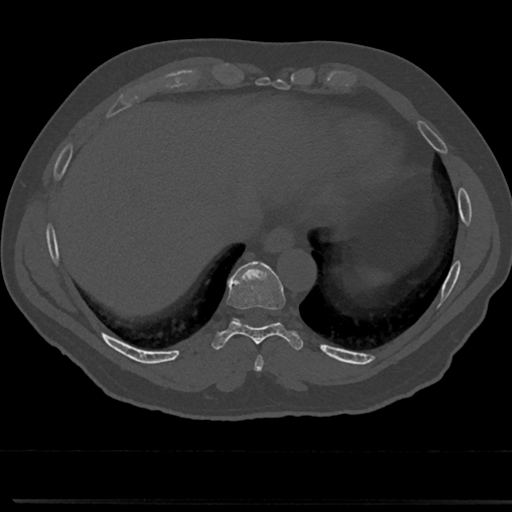
CT including the spine, one axial slice. 120 kVp. Bone window (W 1800 / L 400 HU). 0.5 mm slice thickness. 512 × 512 image matrix, field of view 355 × 355 mm. Patient: male, 61 years. Case-level facts recorded for this patient, not image findings: primary cancer: prostate.
Structures marked on this image (semi-automatically segmented with operator editing):
- T8 vertebra: bounding box [x1, y1, x2, y2] px = [235, 325, 284, 356]
- T9 vertebra: [232, 266, 283, 330]